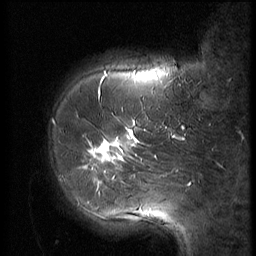
Breast MRI (dynamic contrast-enhanced), one sagittal slice. Position 17 of 56 along the scan axis. 3 images stored at this slice position (order not interpretable as contrast timing). 1.5 T. TE 4.2 ms, TR 9 ms. 2.5 mm slice thickness. 256 × 256 image matrix, field of view 180 × 180 mm. Female patient, age 61 years. From the clinical record (not read from this slice): setting: breast cancer imaged before/during neoadjuvant chemotherapy; receptor status: HR-positive, HER2-negative.
Structures marked on this image (semi-automatic segmentation, software-assisted and operator-edited):
- analysis volume of interest (the breast-tissue region the enhancement analysis was run in; not a lesion): box from (x=47, y=89) to (x=153, y=191) px
- tumour enhancement mask (voxels above the 140 % enhancement threshold inside the analysis volume of interest): (x=85, y=128)–(x=146, y=191)